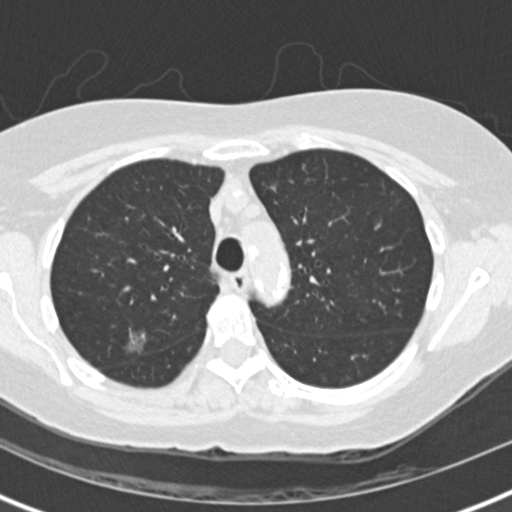
Chest CT (low-dose screening protocol), one axial image. Baseline annual screen. Lung window (W 1500 / L -600 HU). 120 kVp. 512 × 512 image matrix, field of view 300 × 300 mm. Female, age 72 years at enrolment.
• Expert reader's lesion annotation, bounding box [x1, y1, x2, y2] px = [108, 320, 166, 370].
• The exam's reader record, not a measurement of the box and not confirmed to be the same lesion: non-calcified nodule or mass ≥4 mm, right upper lobe, 11 × 11 mm, poorly defined margins, ground glass attenuation.